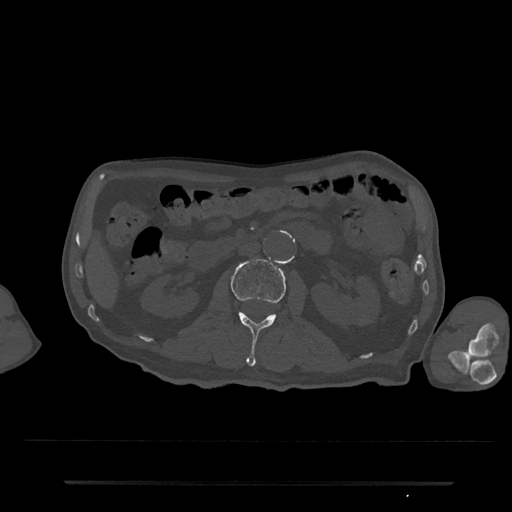
CT including the spine, one axial slice. Position 51 of 797 along the scan axis. Reconstruction kernel Br40s/3. 120 kVp. Bone window (W 1800 / L 400 HU). 0.5 mm slice thickness. 512 × 512 image matrix, field of view 427 × 427 mm. Male patient, age 74 years. From the clinical record (not read from this slice): primary cancer: prostate.
Annotated regions visible in this slice (semi-automatically segmented with operator editing):
- L2 vertebra: box from (x=231, y=259) to (x=286, y=367) px